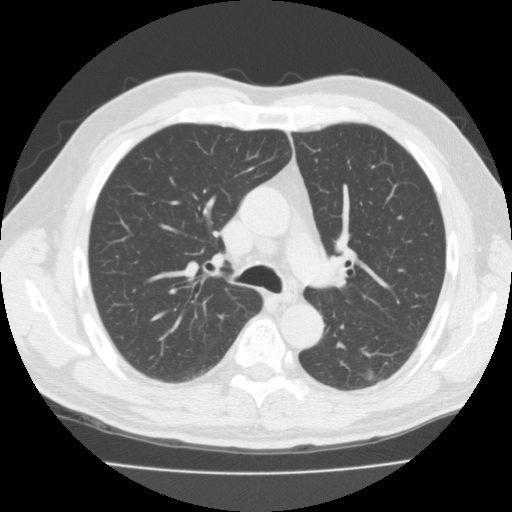
Low-dose screening chest CT, one axial slice; position 65 of 99 along the scan axis; lung window (W 1500 / L -600 HU); 512 × 512 image matrix.
Annotated regions visible in this slice (expert manual segmentation):
- lesion 1 (tumor, lower lobe of left lung): bounding box [x1, y1, x2, y2] px = [369, 375, 372, 380]